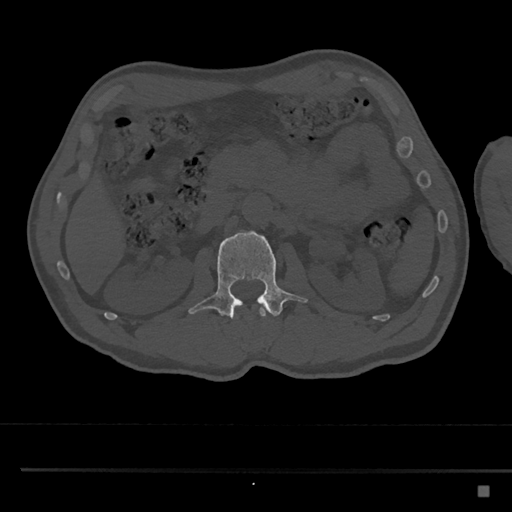
CT including the spine, one axial slice; slice 772 of 797 in the series (ordered by position); bone window (W 1800 / L 400 HU); 0.5 mm slice thickness; 512 × 512 image matrix, field of view 391 × 391 mm. Patient: male, 59 years. Case-level facts recorded for this patient, not image findings: primary cancer: prostate.
Annotated regions visible in this slice (semi-automatically segmented with operator editing):
- L1 vertebra: bounding box <231,310,266,317> (left, top, right, bottom; pixels)
- L2 vertebra: <188,231,309,318>